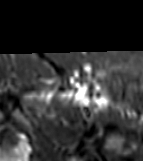
MRI of an extremity soft-tissue mass, one axial slice; slice 56 of 81 in the series (ordered by position); STIR; MR volume resampled by the dataset authors to the PET/CT grid (not the native acquisition matrix); 3.27 mm slice thickness; 143 × 161 image matrix, field of view 140 × 157 mm. Female patient. From the clinical record (not read from this slice): histological type: myxofibrosarcoma; grade: intermediate; site of the primary tumour: left thigh.
Structures marked on this image (expert contour drawn on MRI and transferred to this co-registered scan by the dataset authors):
- gross tumour volume including surrounding oedema: bounding box (x1, y1, x2, y2) in pixels: (37, 81, 112, 107)